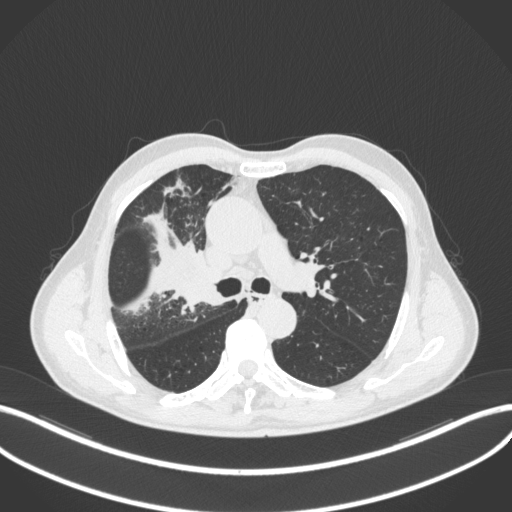
Chest CT, one axial slice; slice 315 of 490 in the series (ordered by position); reconstruction kernel B31f; 120 kVp; lung window (W 1500 / L -600 HU); 512 × 512 image matrix. Male patient, age 69 years. Case-level facts recorded for this patient, not image findings: clinical TNM (as recorded): T2a N0 M0.
Annotated regions visible in this slice (bounding box drawn by a radiologist):
- lung tumour (recorded histology: adenocarcinoma): box from (x=169, y=261) to (x=219, y=314) px